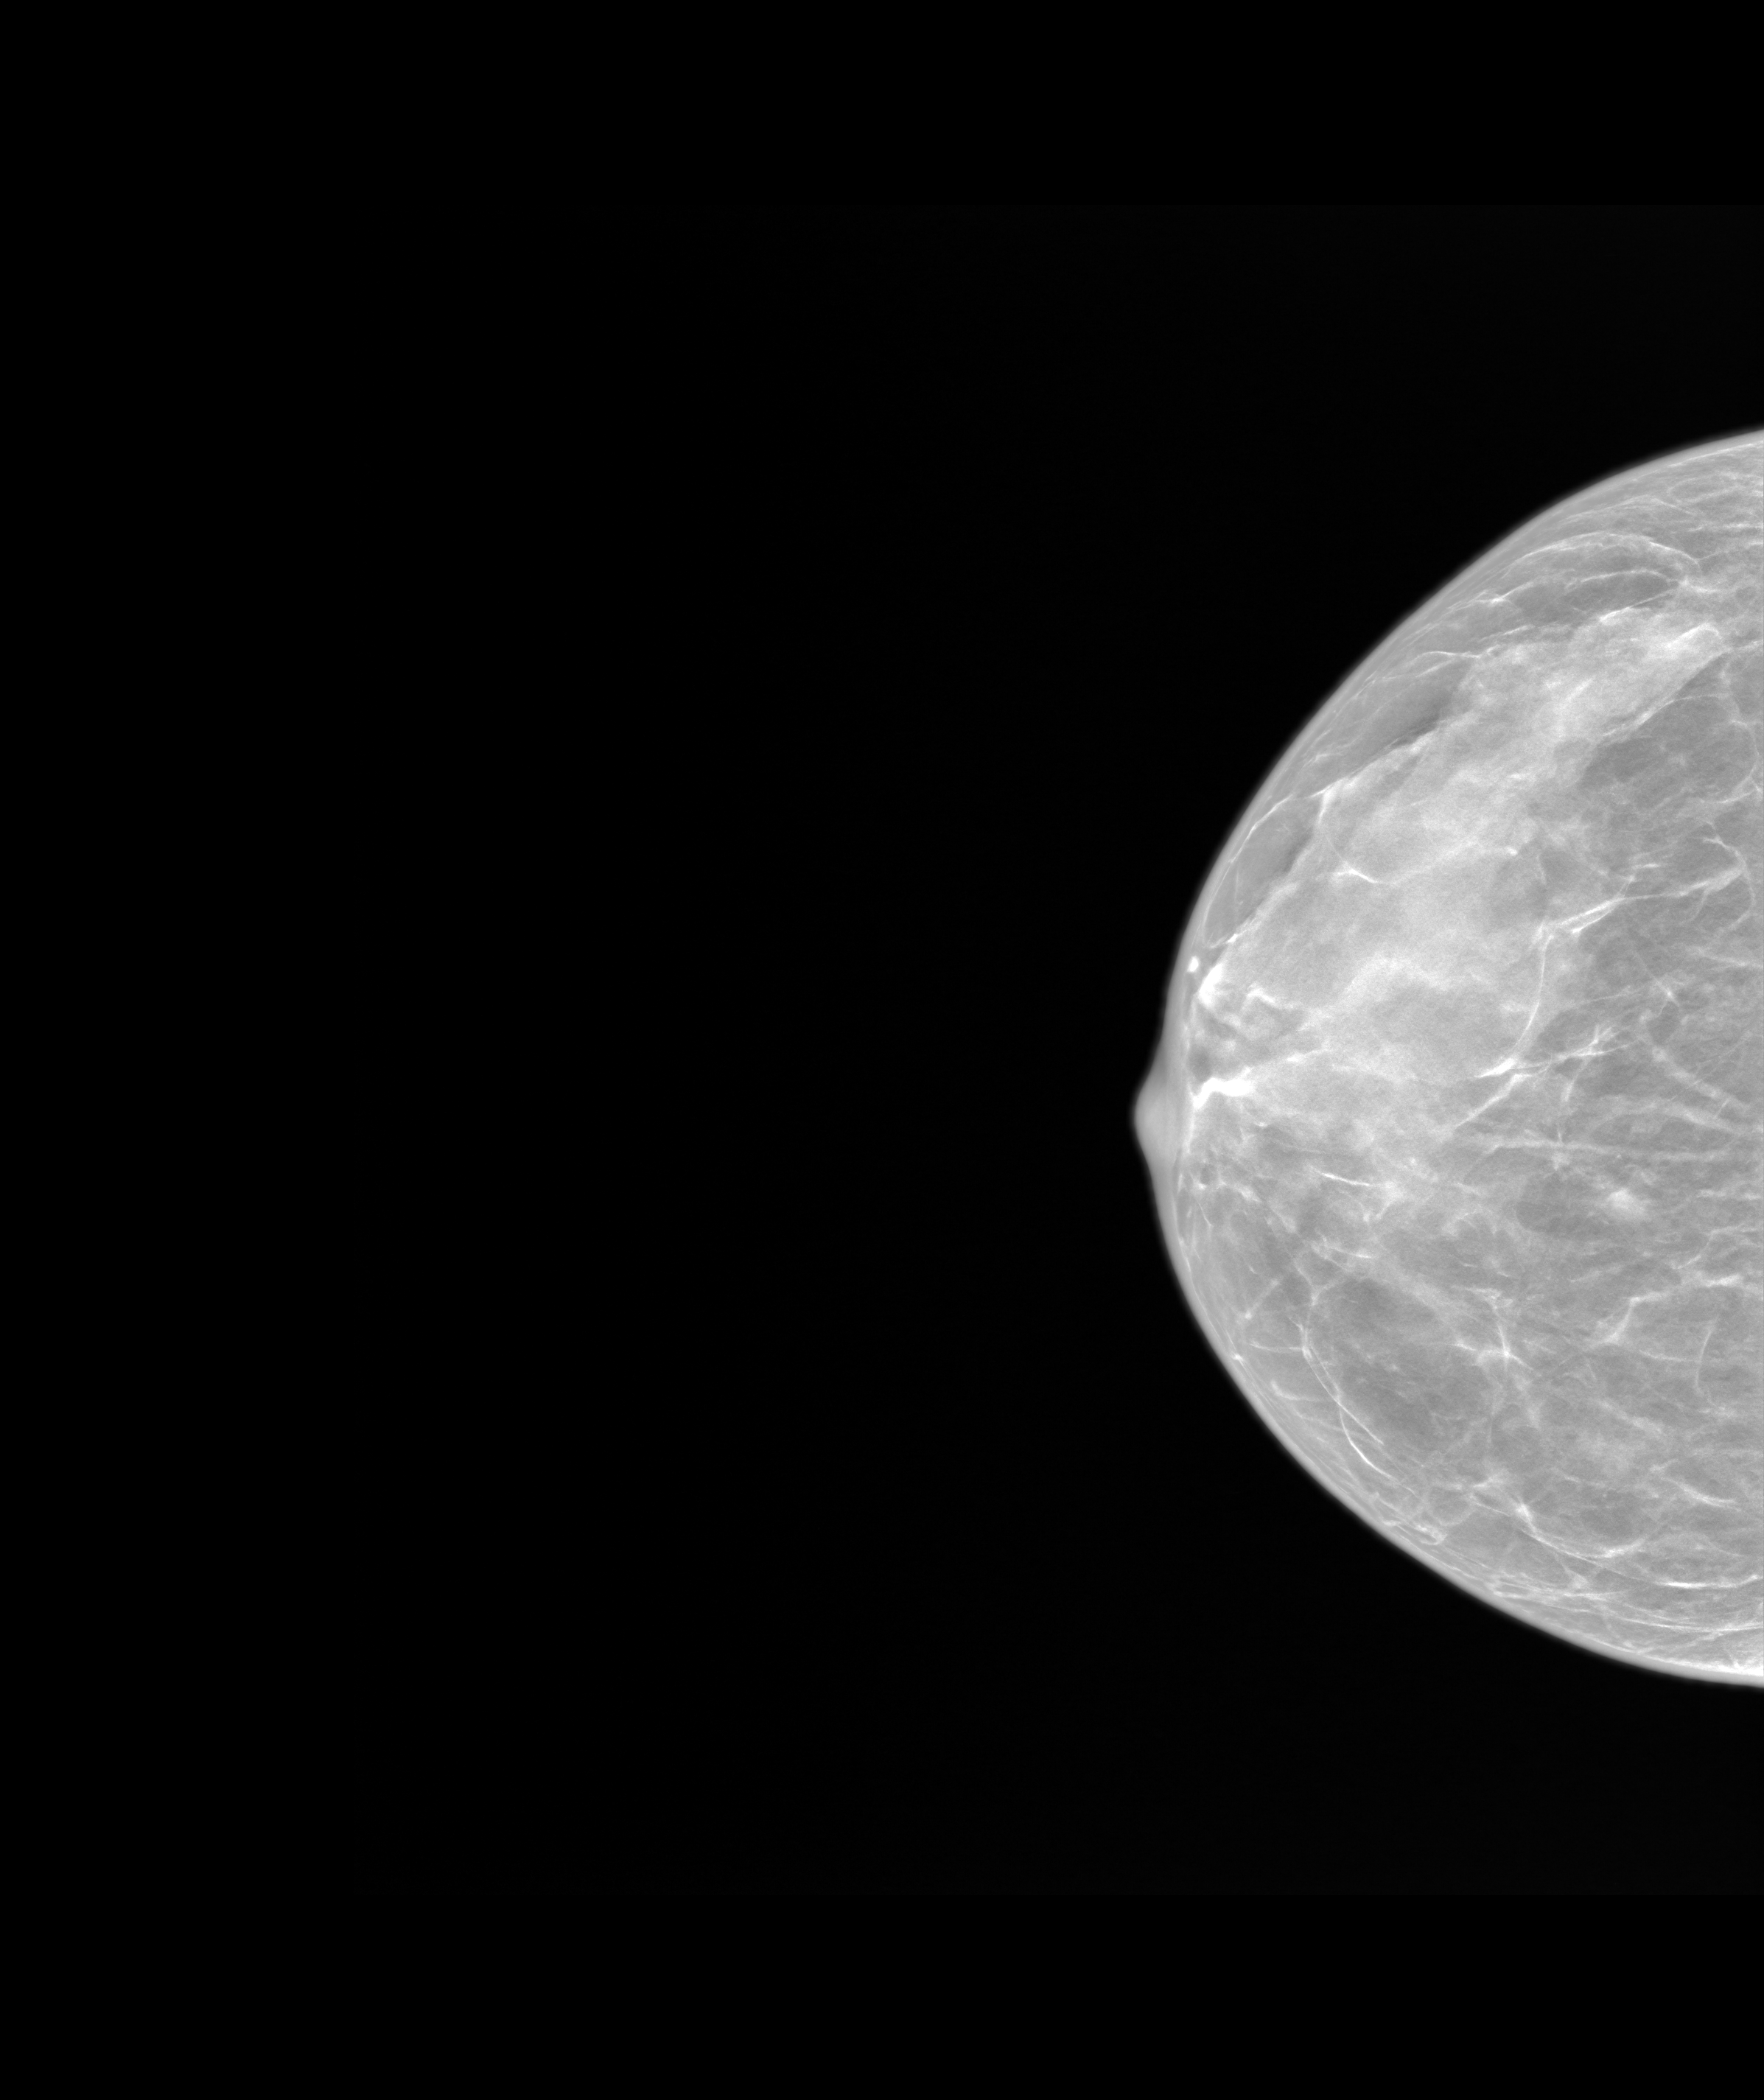
Screening examination. Patient aged 48 years (female).
Image type: synthesized 2-D view from tomosynthesis. Breast: right. Projection: CC view.